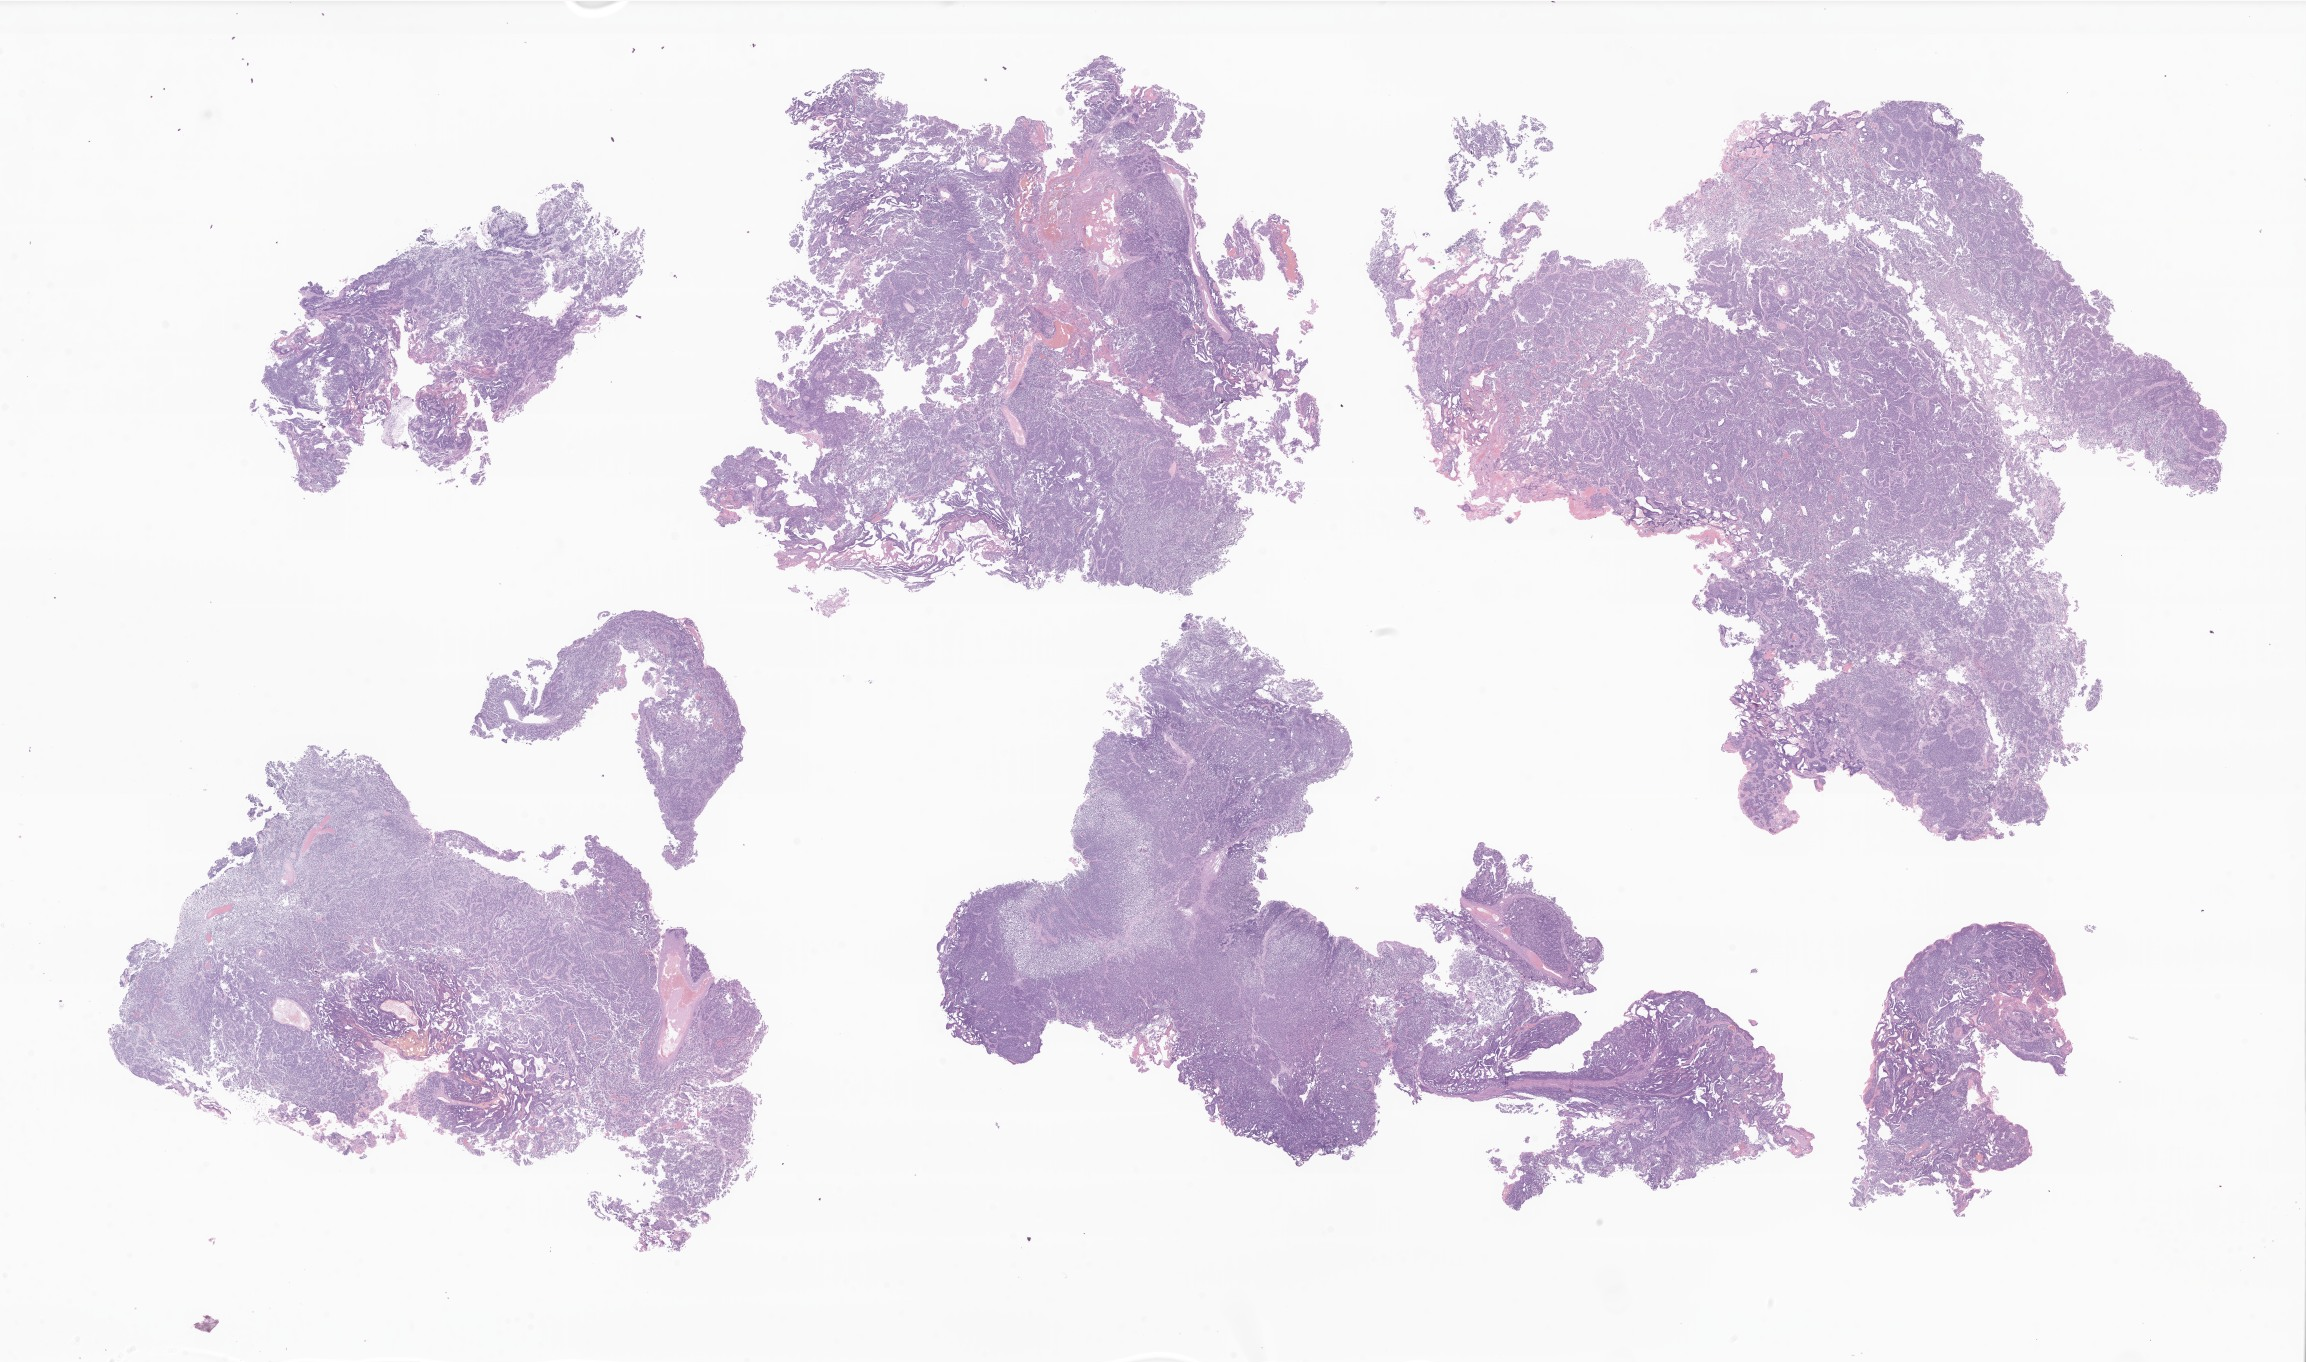
Haematoxylin and eosin whole-slide image of tumor tissue from the pineal gland — whole scanned area (about 38.9 x 23.0 mm) shown as a low-resolution overview; FFPE section. Patient male; age 141 months (11 years 9 months).
Recorded diagnosis: Pineoblastoma.